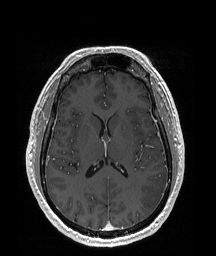
Brain MRI from a brain-tumour surgery series, one axial slice; position 90 of 192 along the scan axis; T1-weighted post-contrast; 1 mm slice thickness; 216 × 256 image matrix, field of view 219 × 260 mm. Case-level facts recorded for this patient, not image findings: histopathology: Glioblastoma; WHO grade: 4; IDH mutation: no; tumour location: Left Temporal Parietal.
Structures marked on this image (outlined manually by an expert reader):
- tumour: bounding box (x1, y1, x2, y2) in pixels: (139, 173, 167, 210)